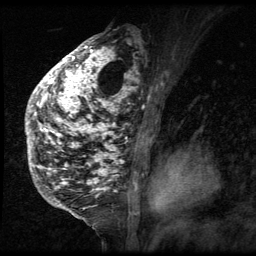
Breast MRI (dynamic contrast-enhanced), one sagittal slice; 3 images stored at this slice position (order not interpretable as contrast timing); 1.5 T; TE 4.2 ms, TR 9 ms; 256 × 256 image matrix. Female patient, age 50 years. Case-level facts recorded for this patient, not image findings: setting: breast cancer imaged before/during neoadjuvant chemotherapy; receptor status: triple-negative.
Structures marked on this image (semi-automatically segmented with operator editing):
- analysis volume of interest (the breast-tissue region the enhancement analysis was run in; not a lesion): bounding box [x1, y1, x2, y2] px = [25, 39, 140, 212]
- tumour enhancement mask (voxels above the 140 % enhancement threshold inside the analysis volume of interest): [25, 39, 140, 212]